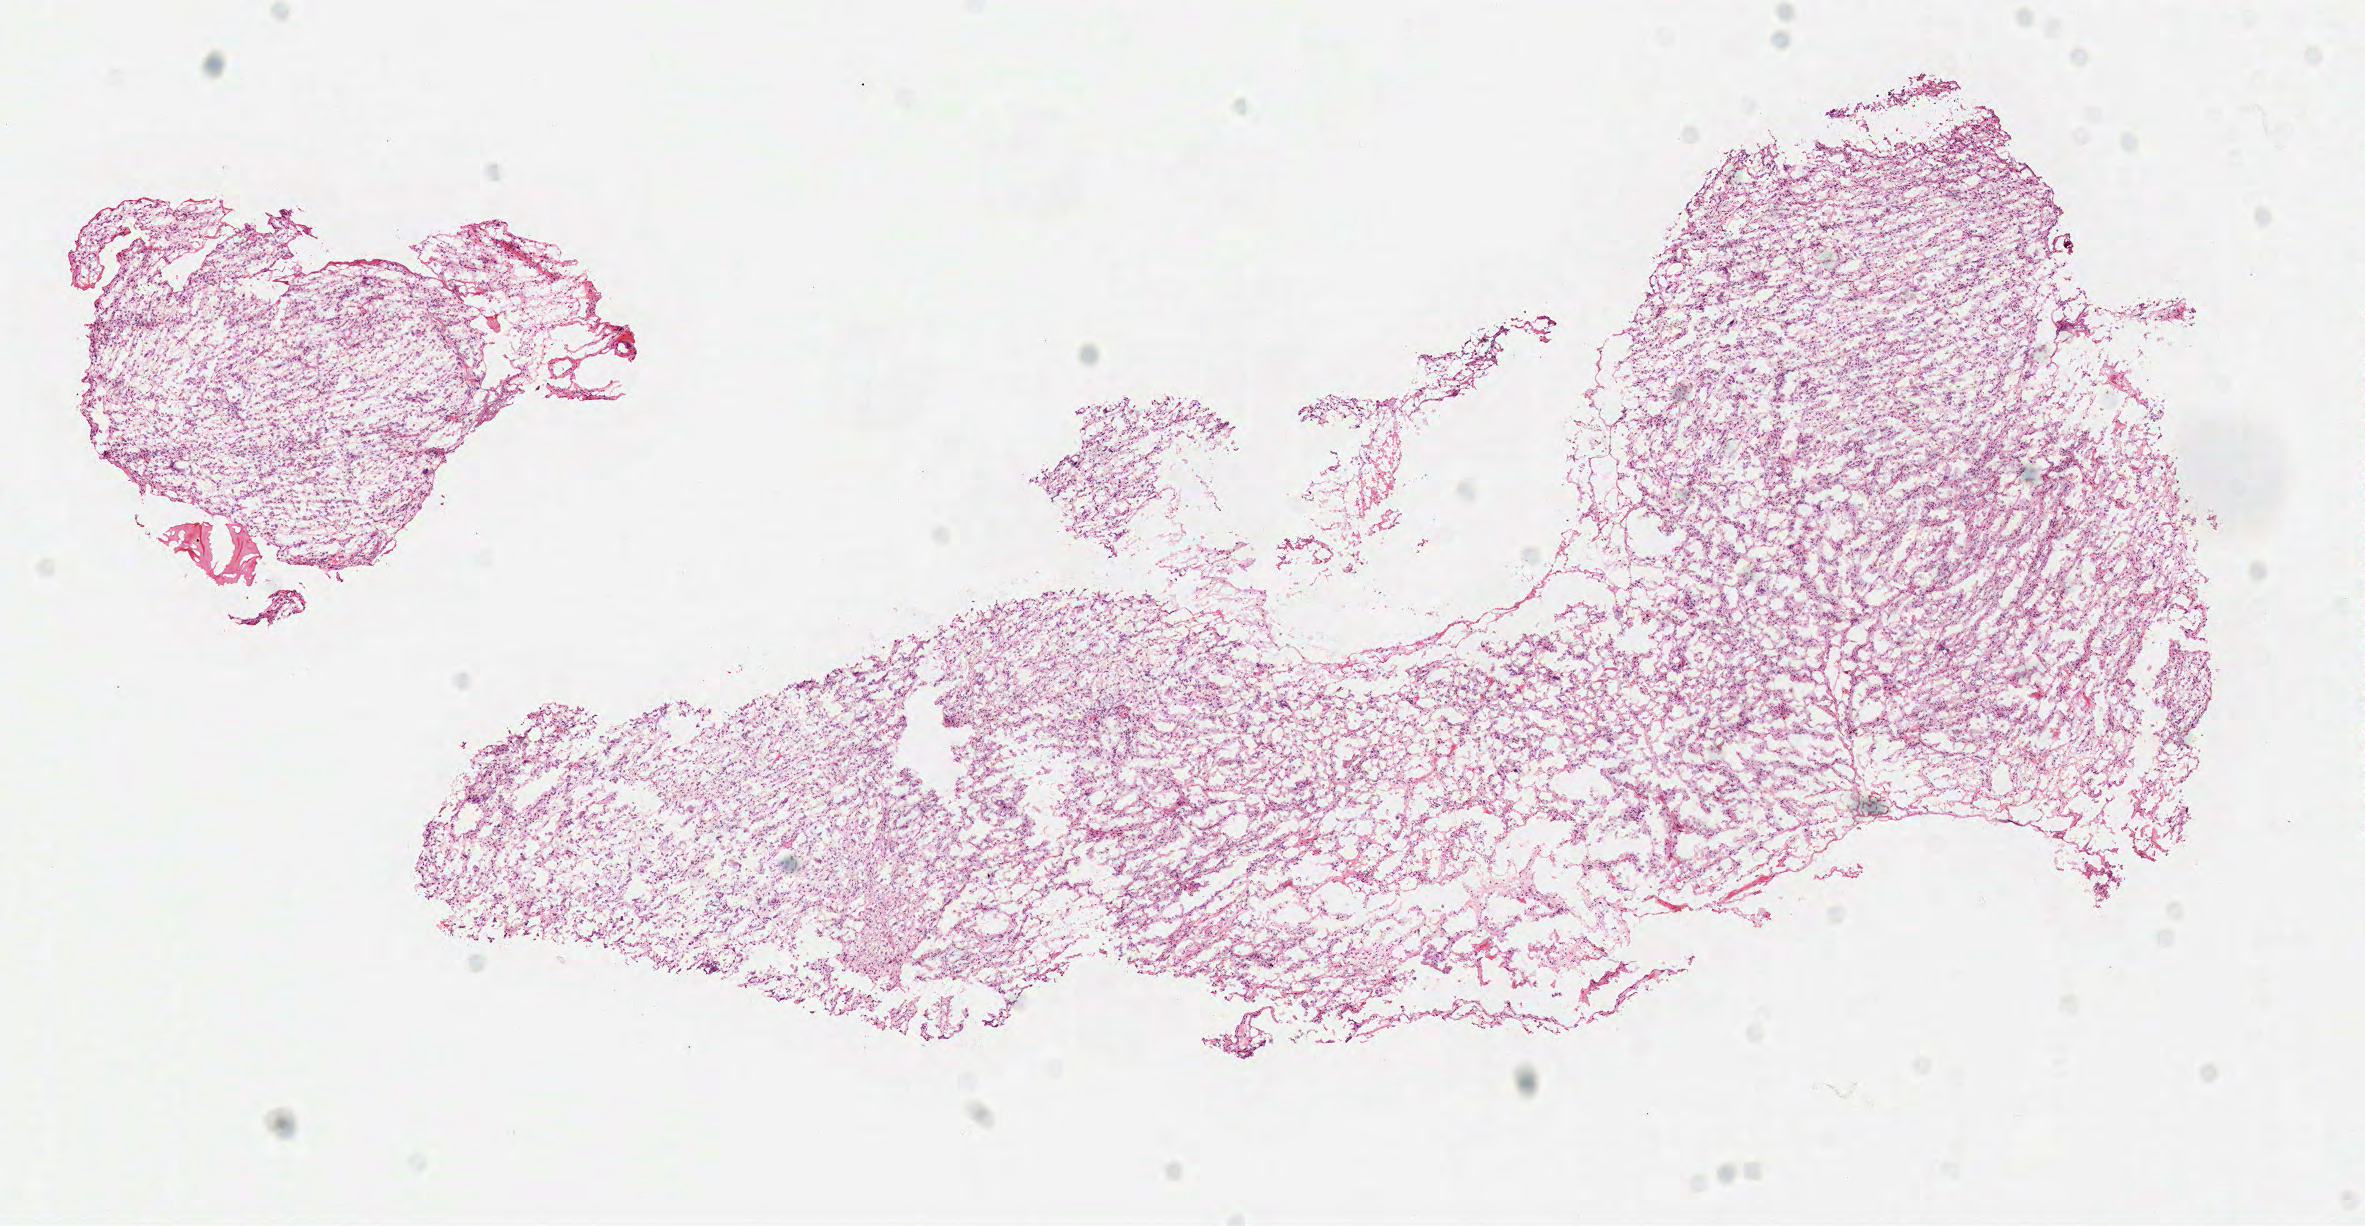
Whole-slide histology image, H&E, whole scanned area (about 9.3 x 4.8 mm, acquisition: 40x scan) shown as a low-resolution overview. Frozen section from the top of the tissue portion. Brain, primary tumour sample. Female, age 47 years at initial diagnosis. Composition of this section per pathologist review: tumour cells 100%, tumour nuclei 75%, normal cells 0%, stromal cells 0%, necrosis 0%.
Histologic diagnosis: Glioblastoma.